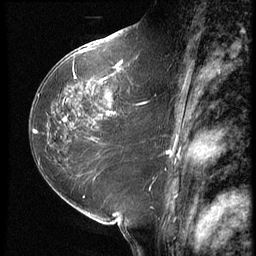
Breast MRI (dynamic contrast-enhanced), one sagittal slice. Slice 34 of 64 in the series (ordered by position). 3 images stored at this slice position (order not interpretable as contrast timing). 1.5 T. TE 4.2 ms, TR 9 ms. 2.5 mm slice thickness. 256 × 256 image matrix, field of view 180 × 180 mm. Female patient, age 59 years. Case-level facts recorded for this patient, not image findings: setting: breast cancer imaged before/during neoadjuvant chemotherapy; receptor status: HER2-positive.
Outlined on this slice (semi-automatic segmentation, software-assisted and operator-edited):
- analysis volume of interest (the breast-tissue region the enhancement analysis was run in; not a lesion): bounding box (x1, y1, x2, y2) in pixels: (54, 65, 155, 132)
- tumour enhancement mask (voxels above the 140 % enhancement threshold inside the analysis volume of interest): (63, 65, 140, 121)